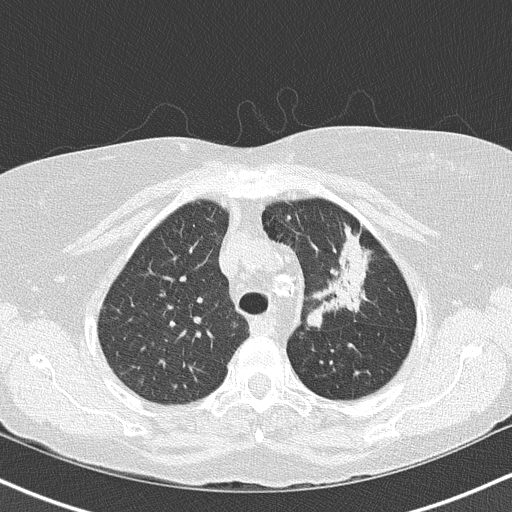
Low-dose screening chest CT, axial slice, third screening round (two years after baseline), lung window (W 1500 / L -600 HU), 2 mm slice thickness, lung (sharp) reconstruction kernel (B50f), 120 kVp, slice 116 of 147 in the series. Female, age 68 years at enrolment. Former smoker at enrolment.
Expert reader's lesion annotation, bounding box (x1, y1, x2, y2) in pixels: (297, 219, 382, 327). Screening reader's record for this exam (one nodule recorded; not confirmed to be the boxed lesion): non-calcified nodule or mass ≥4 mm, left upper lobe, 5 × 5 mm, poorly defined margins, mixed attenuation, pre-existing on the prior screen: yes; interval growth: yes. Official screen result: positive, other. Participant outcome: lung cancer diagnosed 42 days after this screen — adenocarcinoma, NOS, left upper lobe, poorly differentiated (G3), stage IB (AJCC 6th edition), 50 mm at pathology.